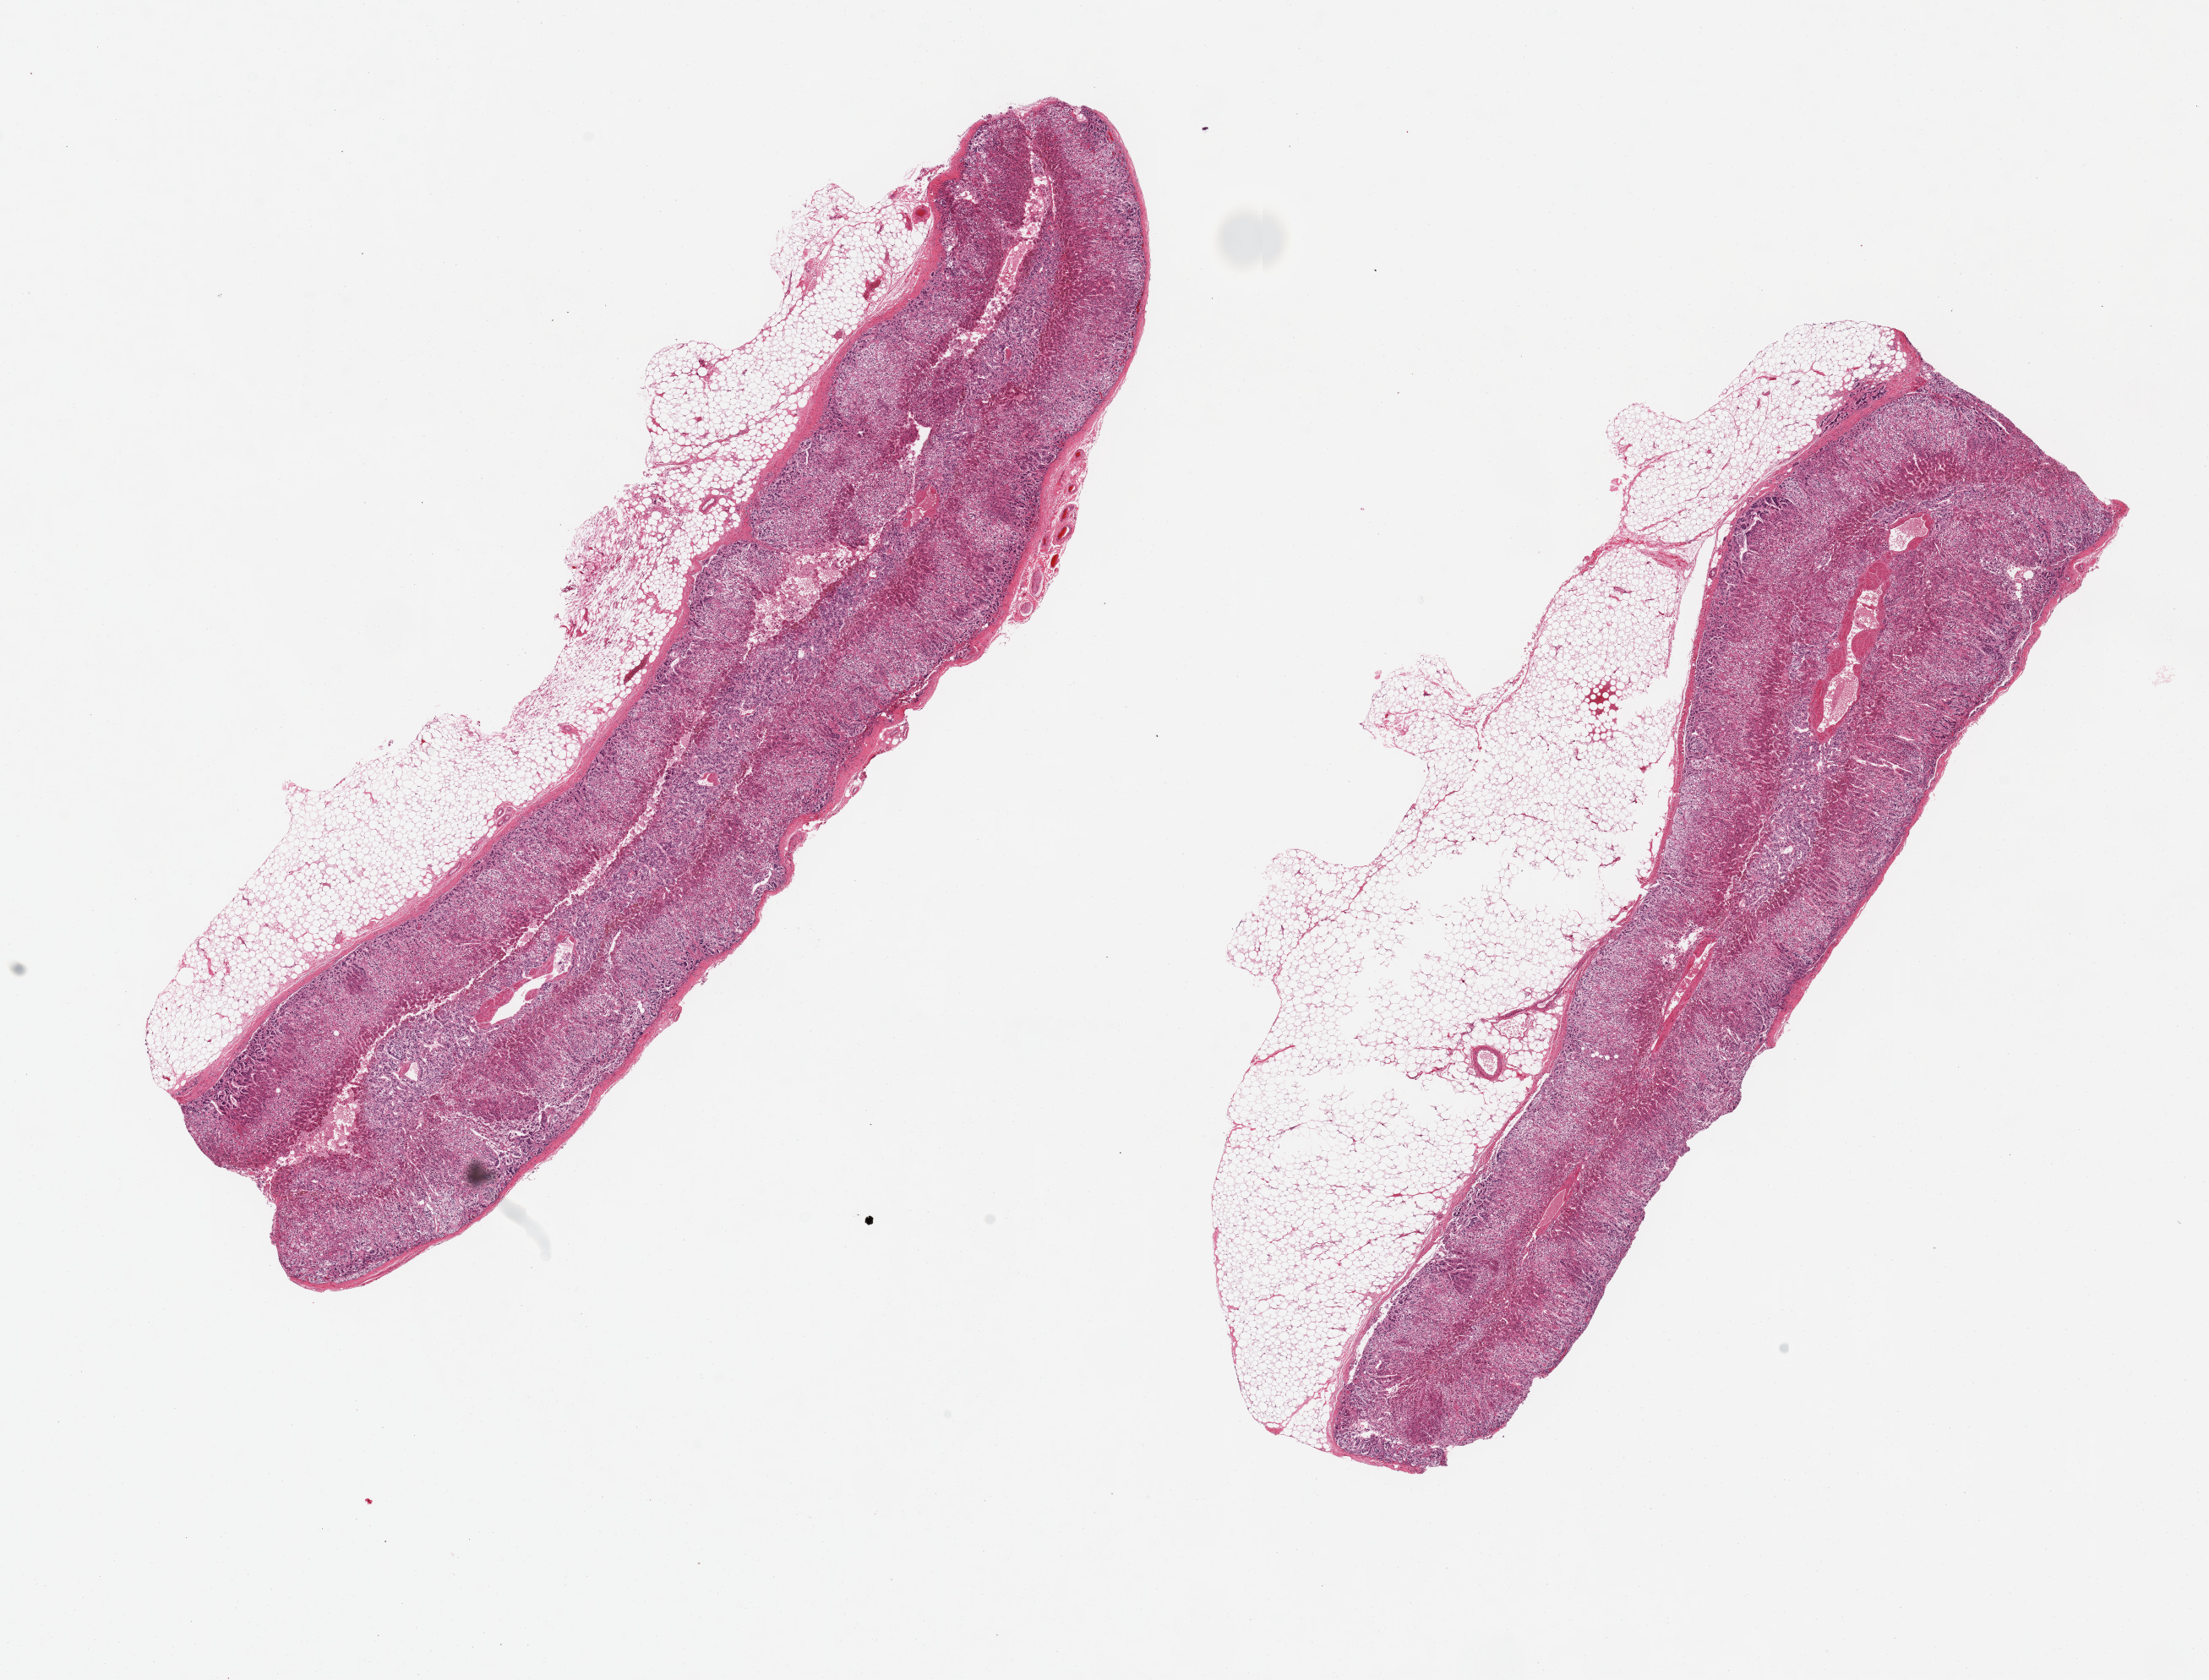
H&E whole-slide image — whole scanned area (about 20.7 x 15.7 mm) shown as a low-resolution overview; PAXgene-fixed, paraffin-embedded tissue; target tissue: adrenal gland; donor tissue sample. Donor: male.
Pathologist's review note for this sample: 2 ~12x3.5mm aliquots. Adherent 1mm layer of fat on both.